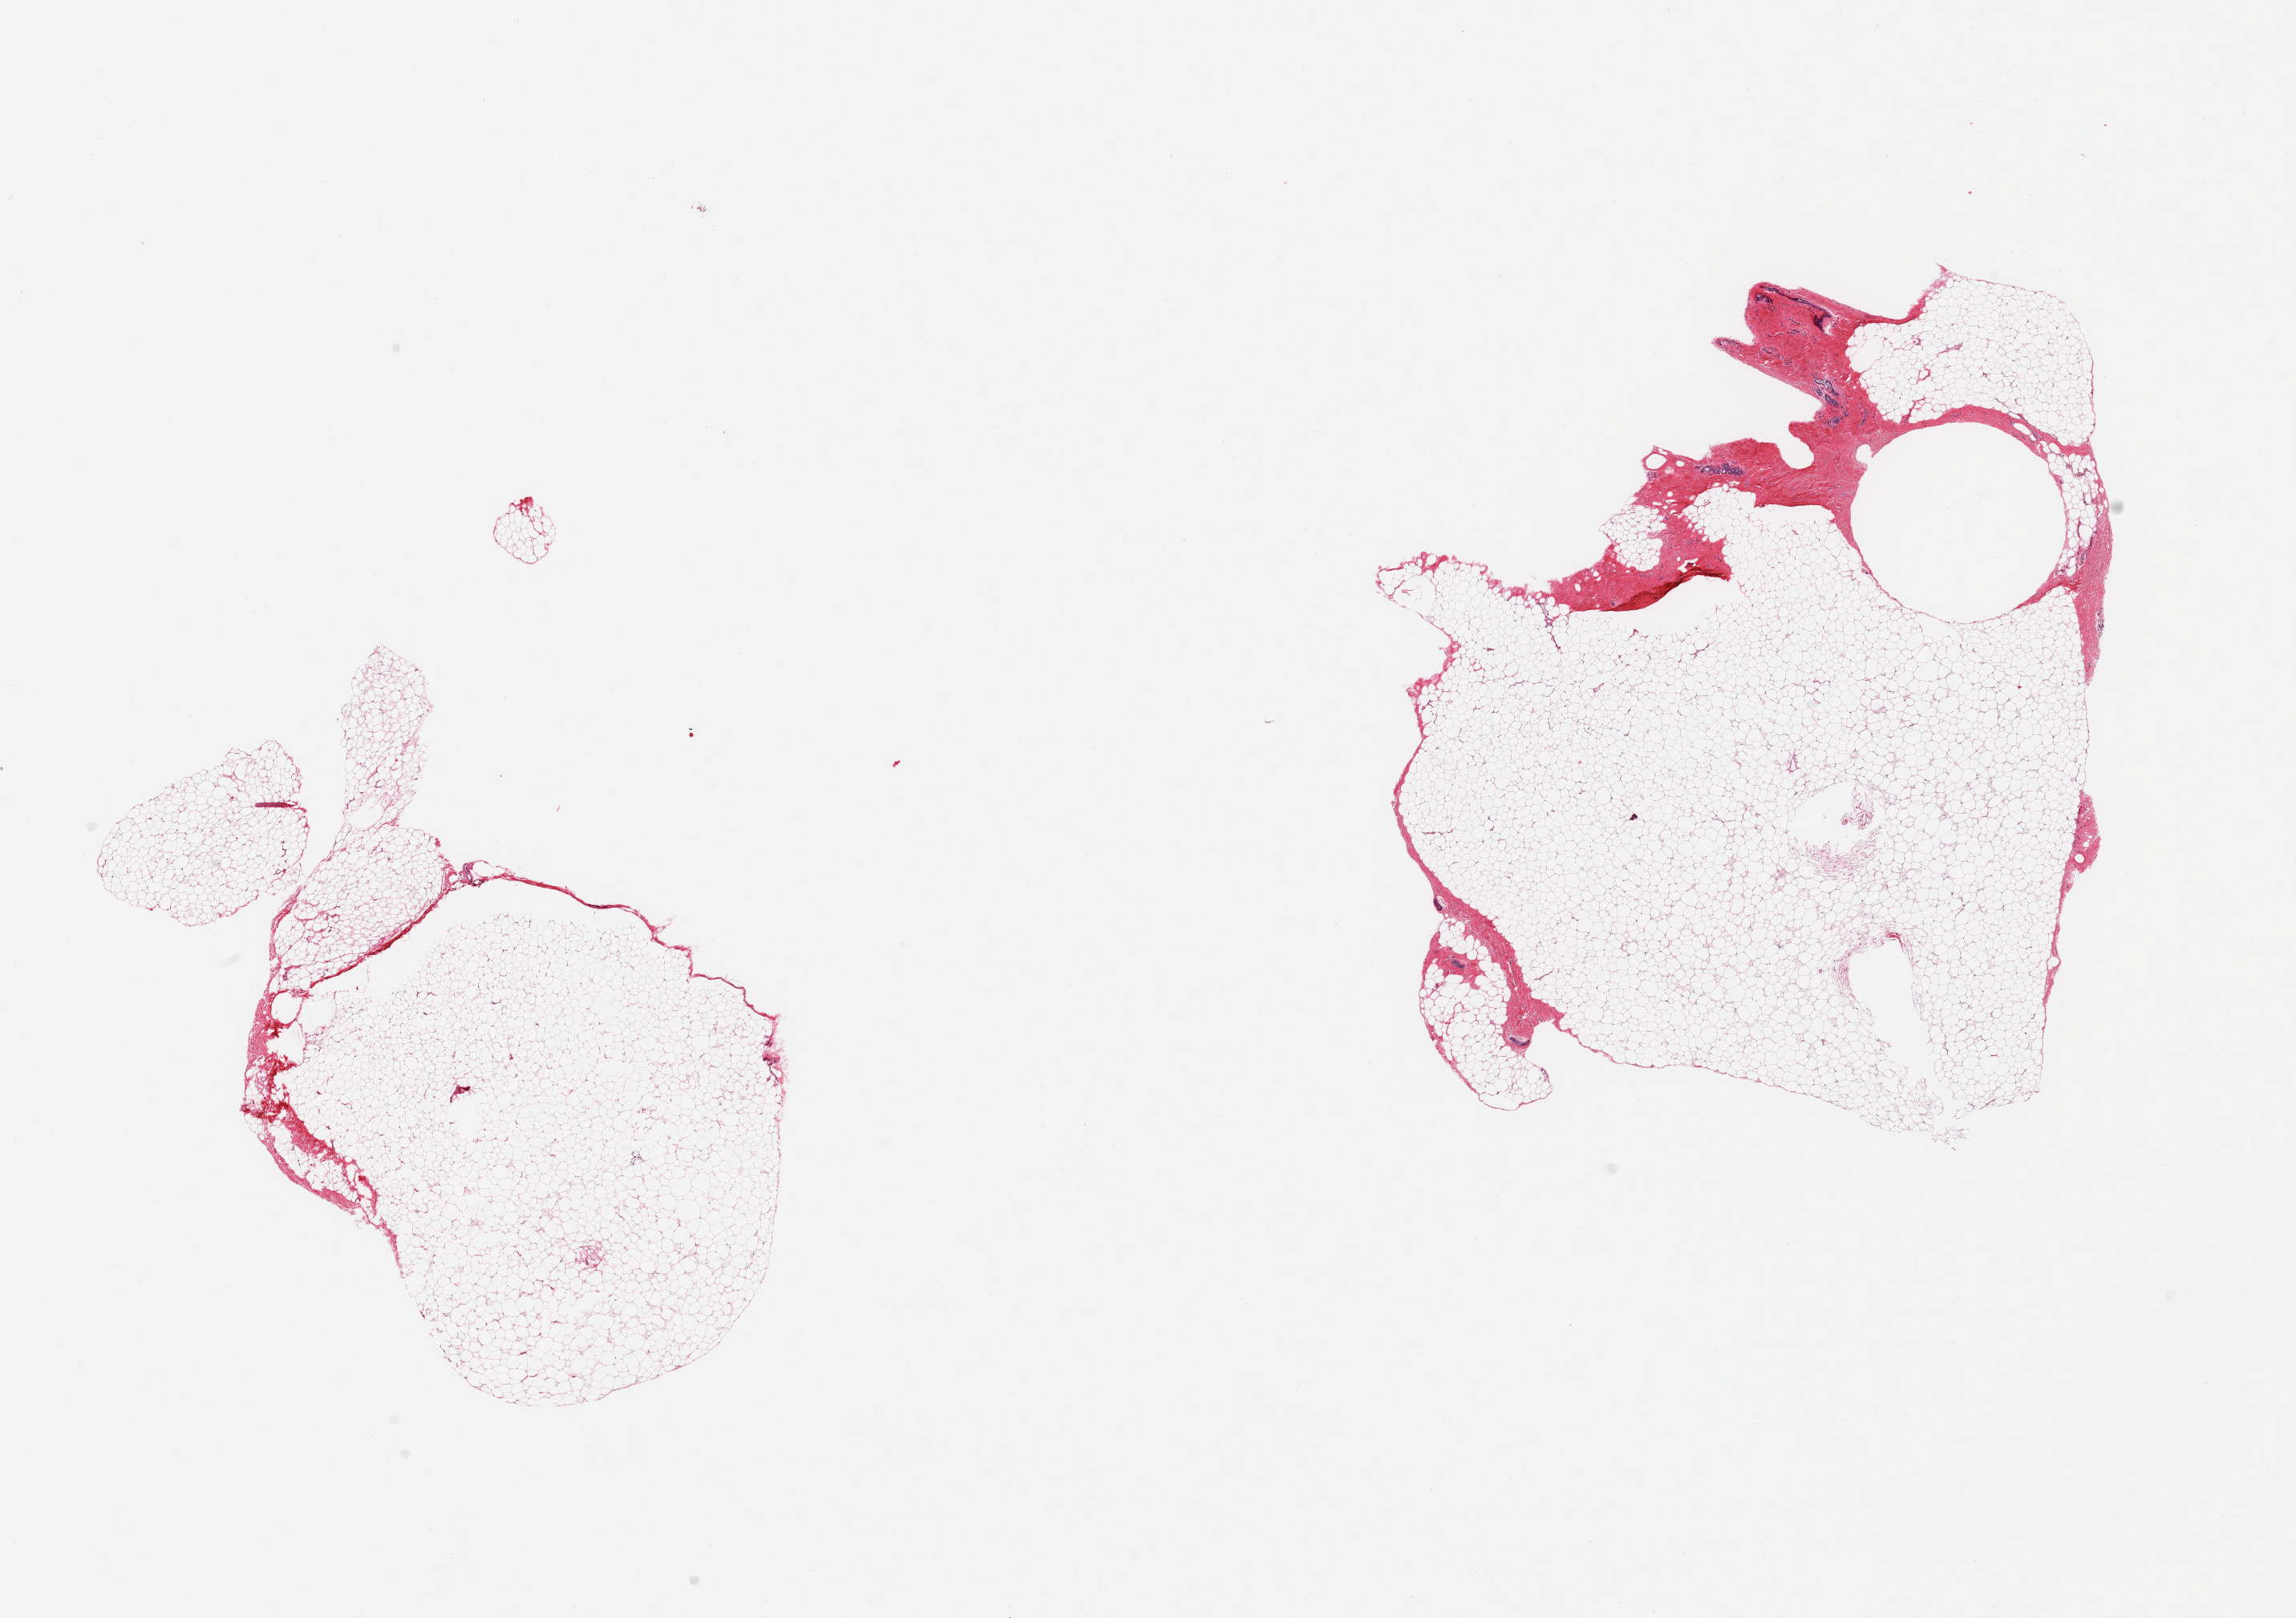
Whole-slide image, H&E stain, brightfield — low-resolution overview of the scanned area, about 22.6 x 16.0 mm; PAXgene-fixed paraffin-embedded (PFPE) section; target tissue: breast; donor tissue sample. Donor sex: male.
Pathologist's review note for this sample: 2 pieces, mainly fibroadipose elements; few minute ductal elements.